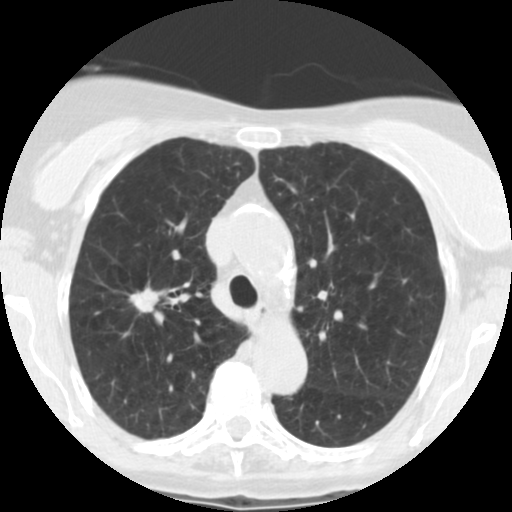
Chest CT (low-dose screening protocol), one axial image, baseline annual screen, lung window (W 1500 / L -600 HU), 120 kVp, slice 176 of 246 in the series, 512 × 512 image matrix, field of view 288 × 288 mm. Female participant, aged 67 years at enrolment.
Expert-annotated lung lesion, bounding box (x1, y1, x2, y2) in pixels: (114, 280, 173, 322). The screening reader recorded 6 non-calcified nodules or masses ≥4 mm on this exam (right upper lobe, right middle lobe, left lower lobe, right middle lobe, left lower lobe, left lower lobe); which of them this box marks is not recorded. Official screen result: positive, change unspecified: nodule(s) >= 4 mm or enlarging nodule(s), mass(es), or other non-specific abnormalities suspicious for lung cancer. Later outcome: lung cancer diagnosed 15 days after this screen — adenocarcinoma, NOS, right upper lobe, moderately differentiated (G2), stage IA (AJCC 6th edition), 14 mm at pathology.